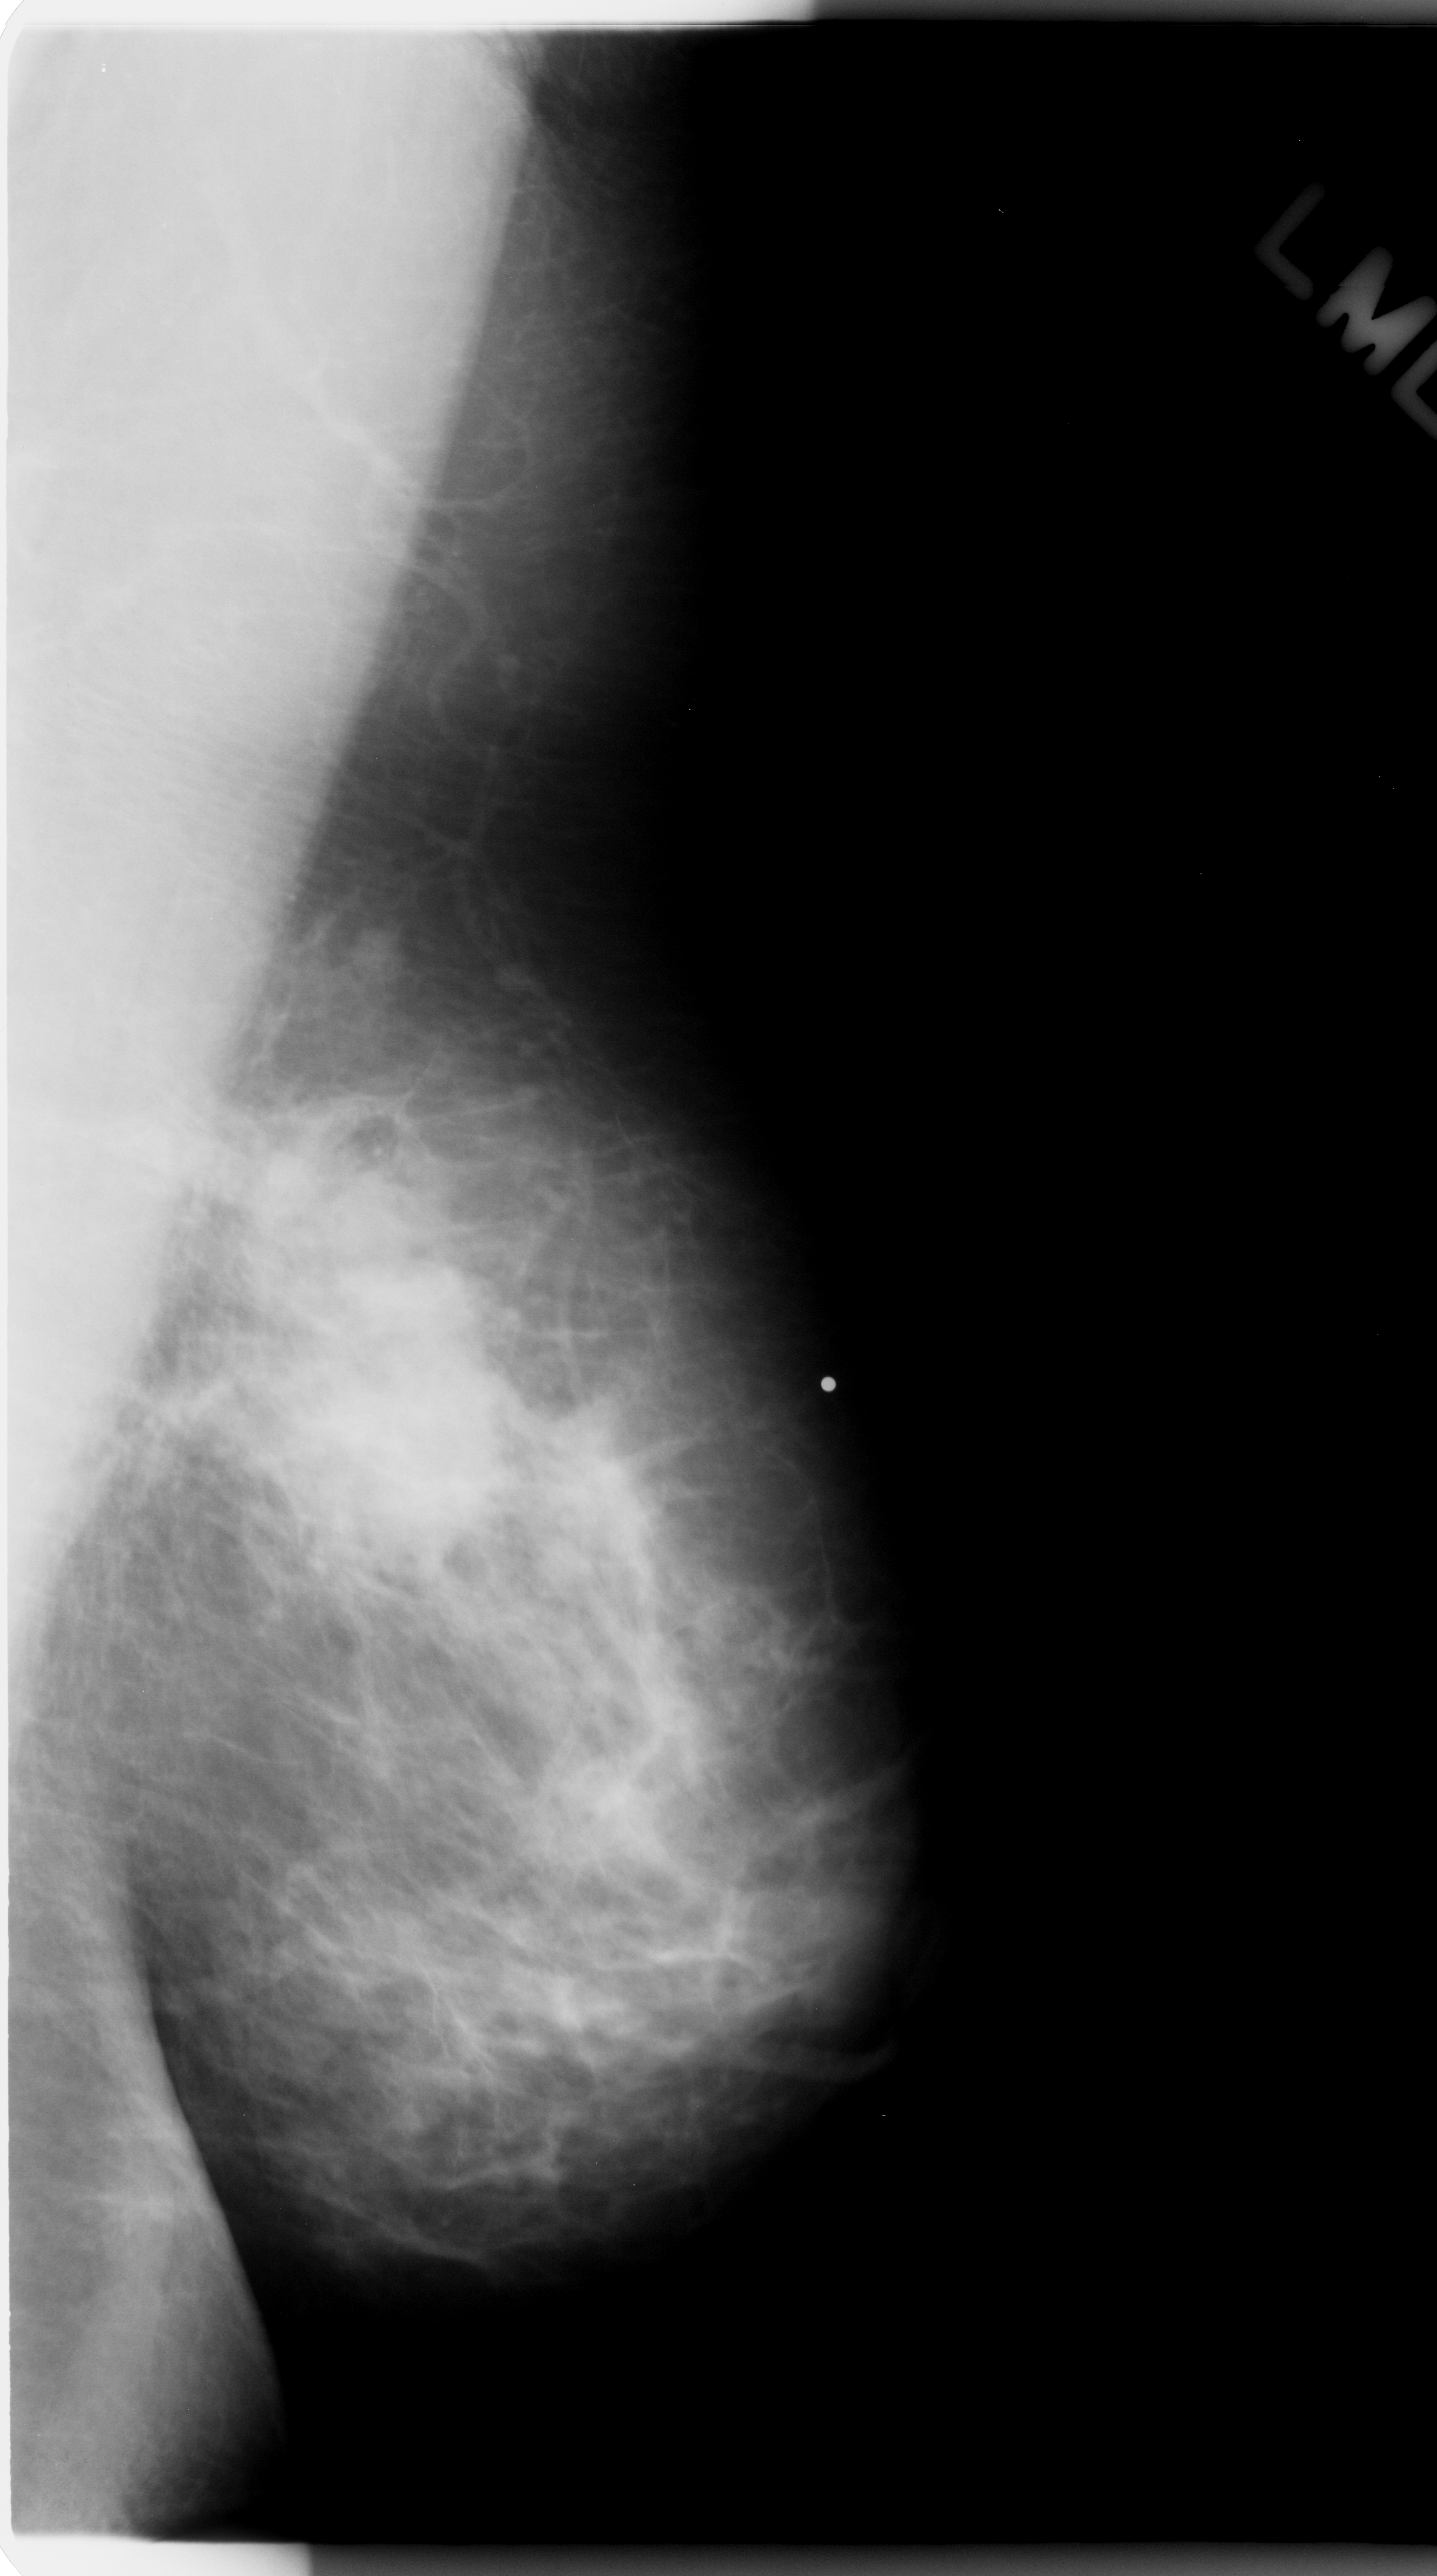
Mammogram (digitized film). Left breast. Mediolateral oblique (MLO) view. Breast composition: scattered fibroglandular densities (BI-RADS density category 2 of 4). 1437 × 2576 image matrix.
Marked abnormalities (boxes around the expert regions of interest):
- mass, shape irregular, margins ill defined; BI-RADS assessment category 5; pathology (as recorded): malignant: bounding box [x1, y1, x2, y2] px = [238, 1221, 582, 1617]